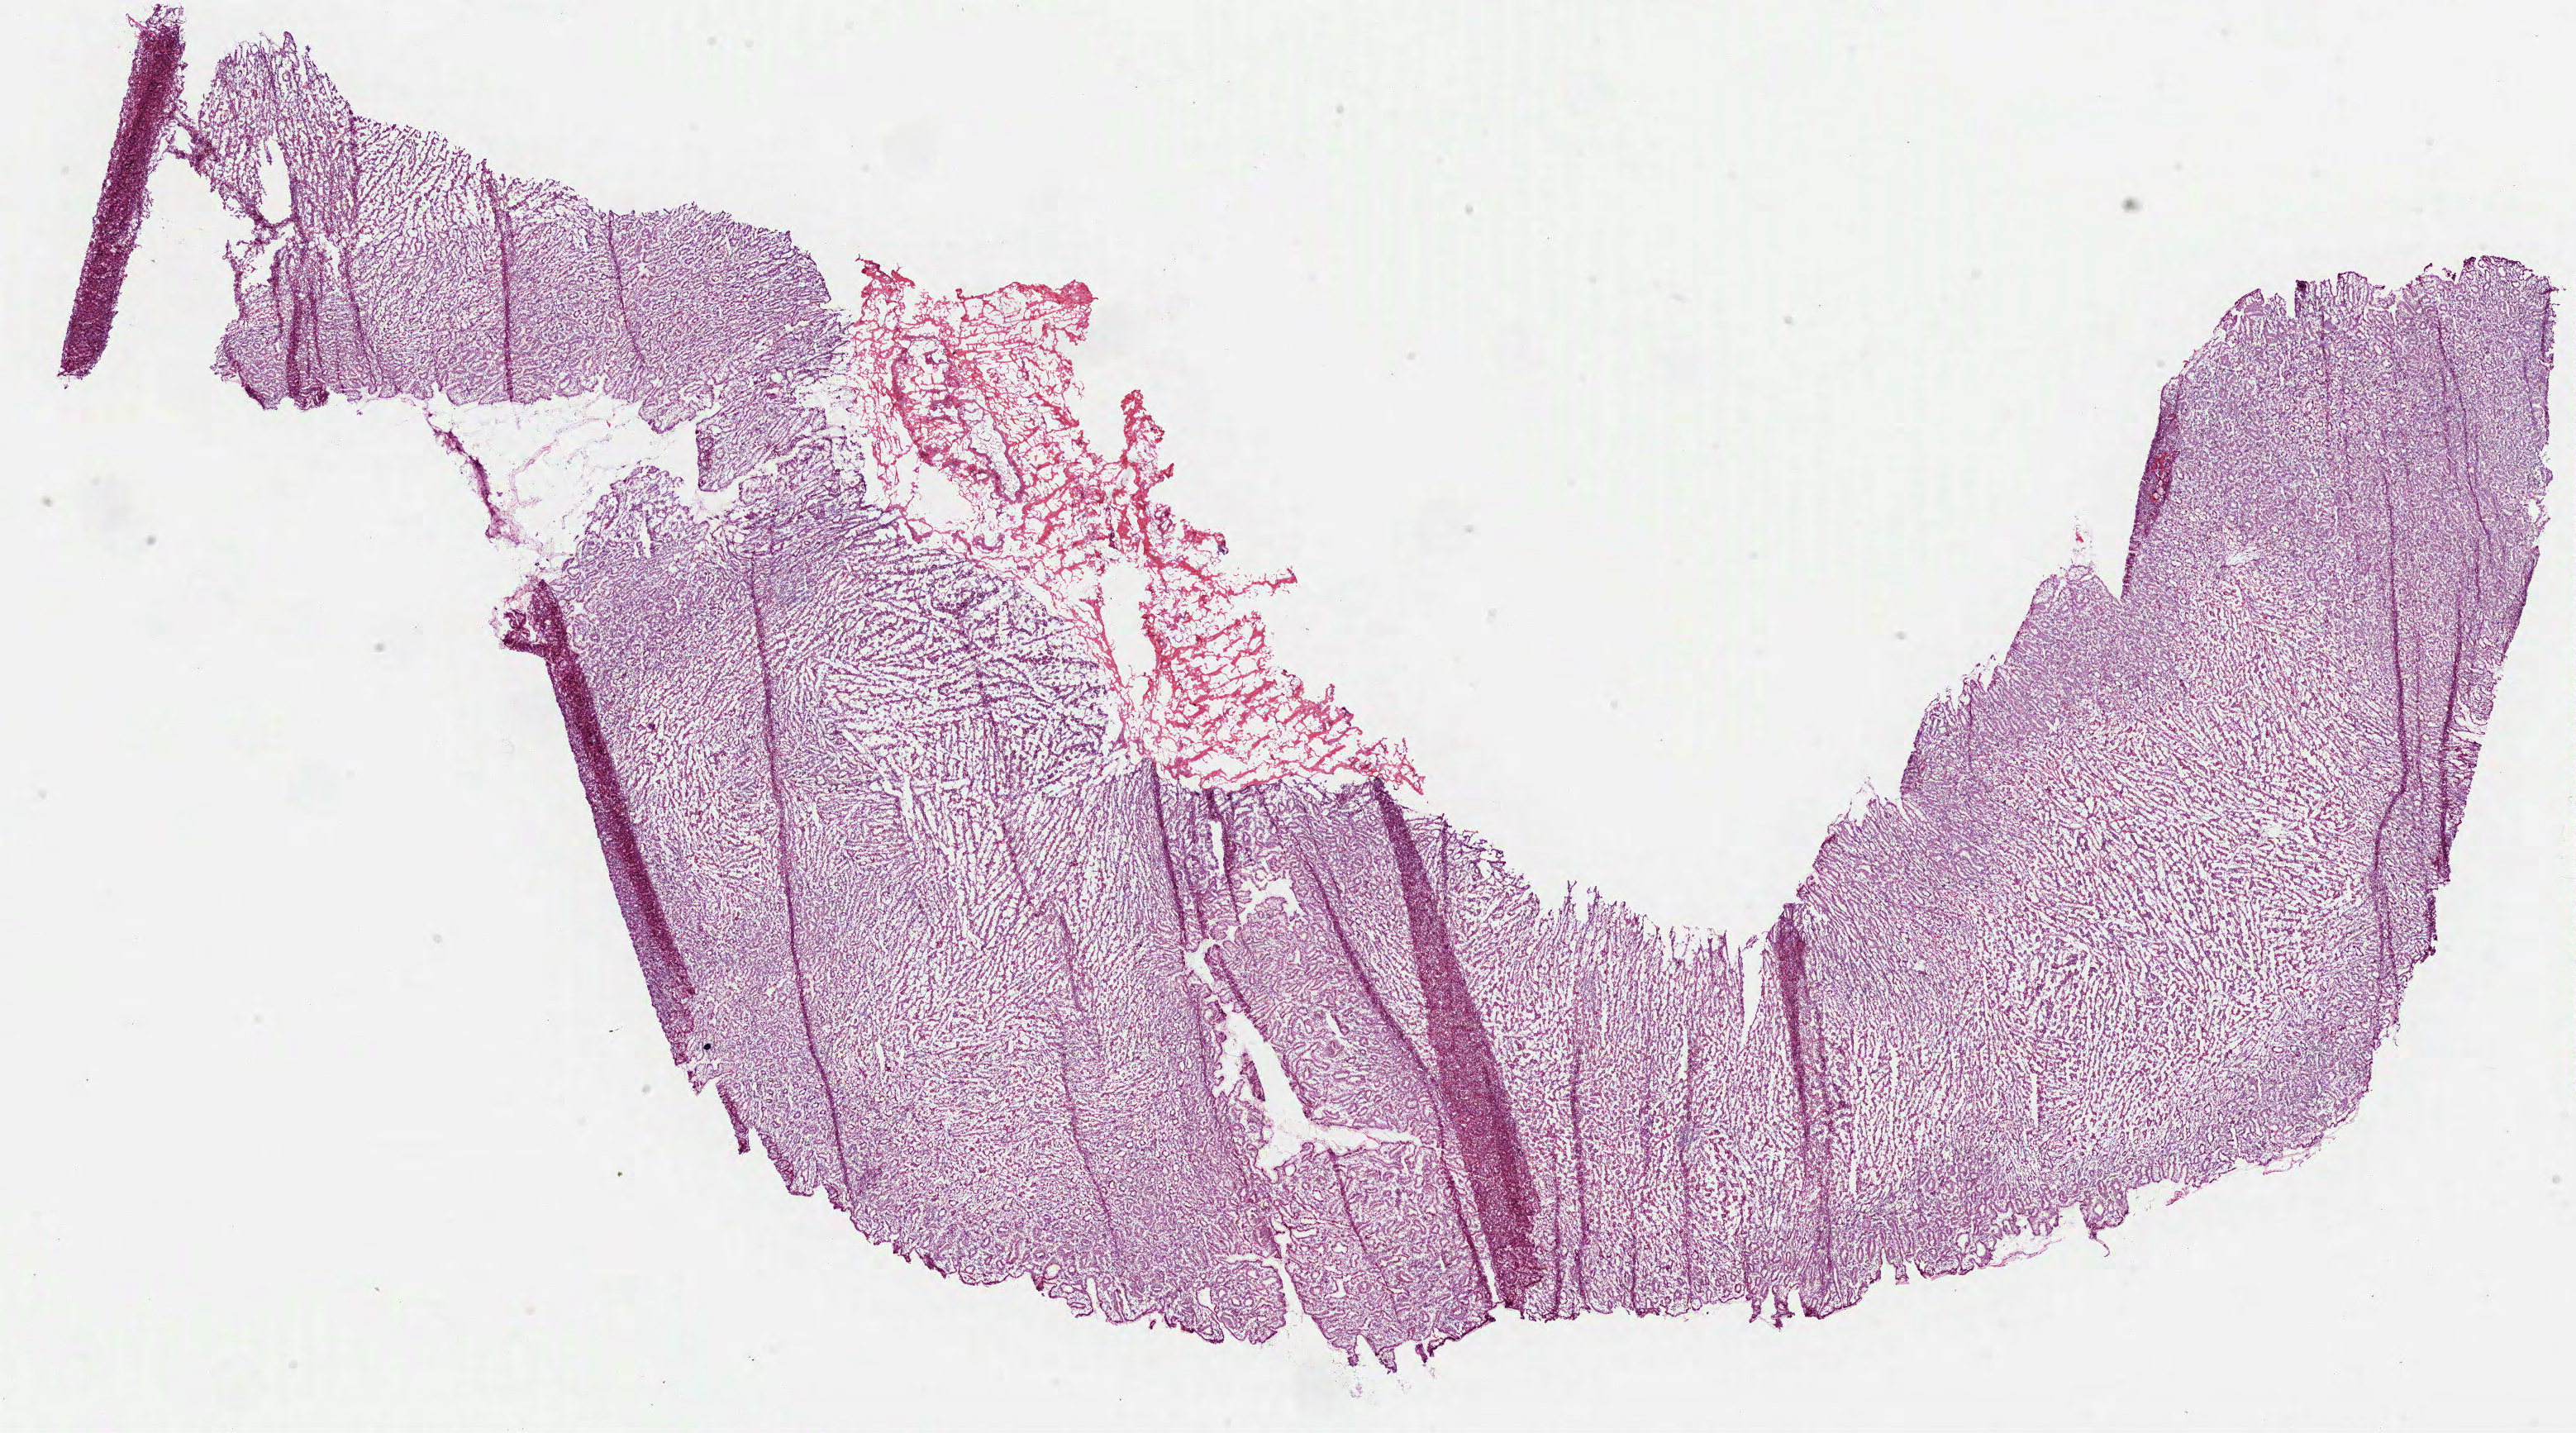
Digitized H&E-stained tissue section (whole slide) — shown as a low-resolution overview of the whole scanned area (about 25.1 x 14.0 mm, acquisition: 40x scan), frozen section from the top of the tissue portion, solid tissue normal (non-tumour tissue) sample from the stomach. Patient: male, age at initial diagnosis 81 years.
This section: solid tissue normal (non-tumour) sample from the same patient. Patient diagnosis: Papillary adenocarcinoma, NOS (body of stomach).